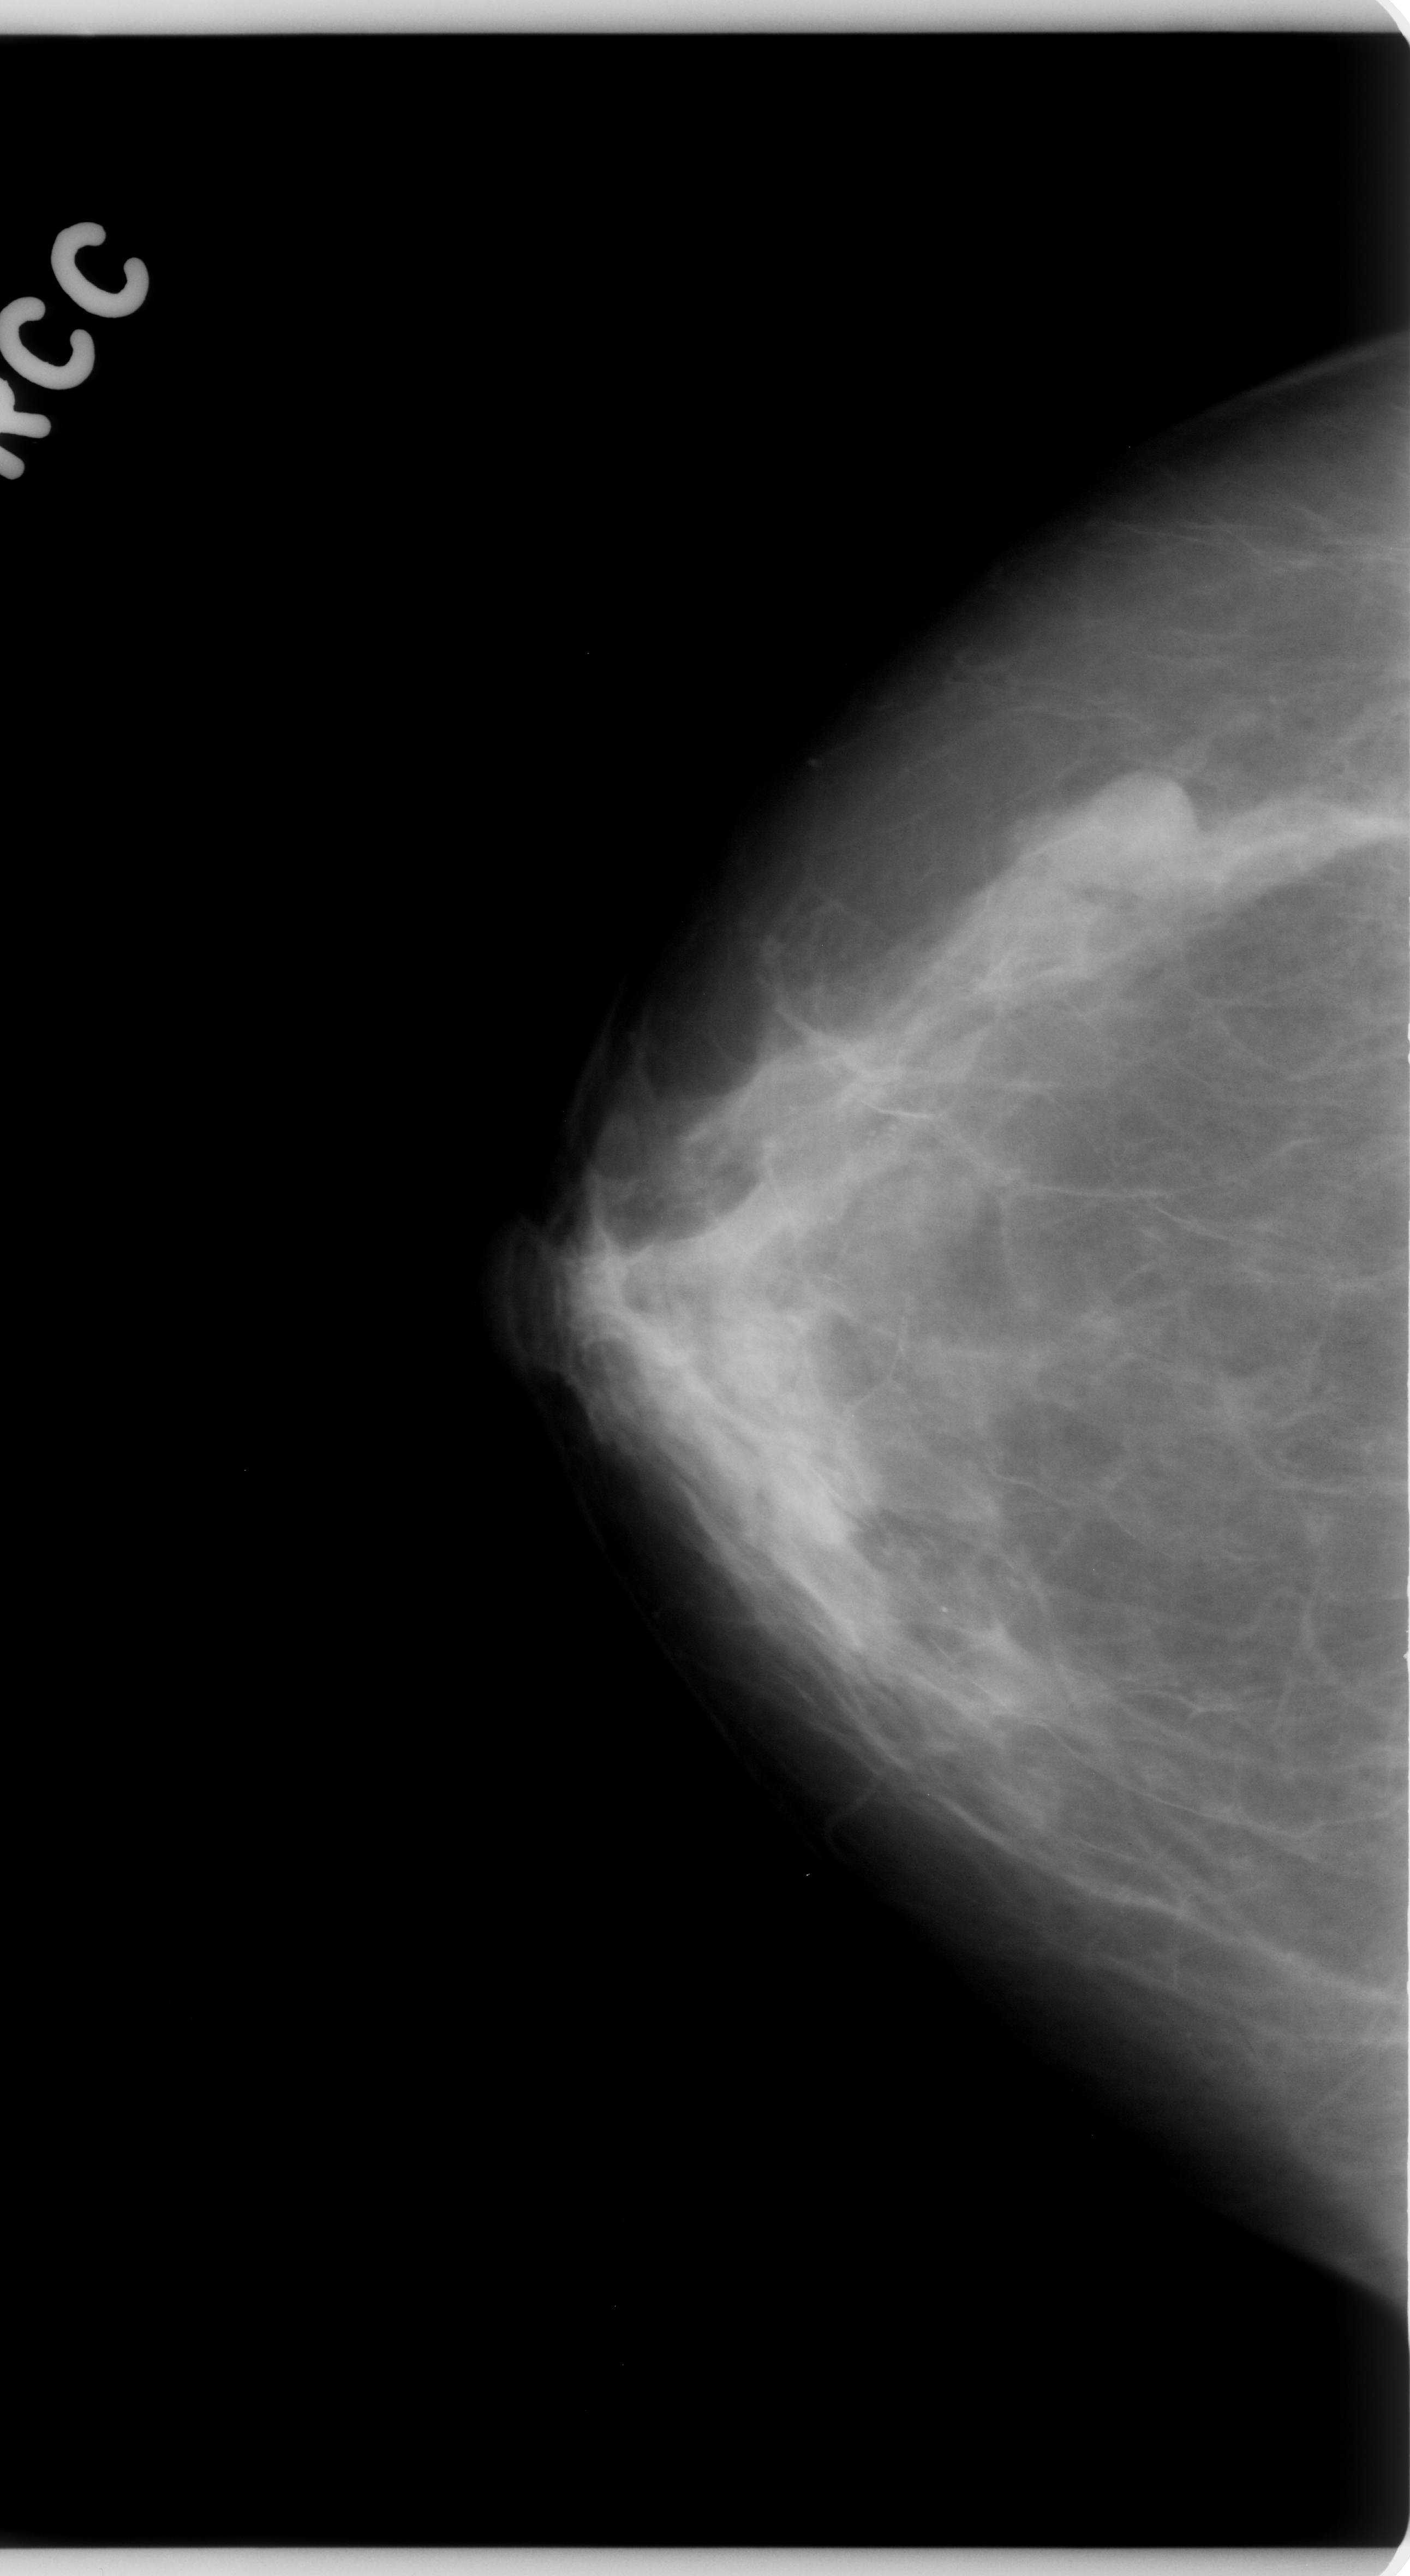
Scanned film-screen mammogram; right breast; CC view.
Marked findings (only marked abnormalities are described; nothing is implied about the rest of the image): mass, shape oval, margins circumscribed; BI-RADS assessment category 4; subtlety rating 5 on a 1 (subtle) to 5 (obvious) scale; pathology (as recorded): benign.